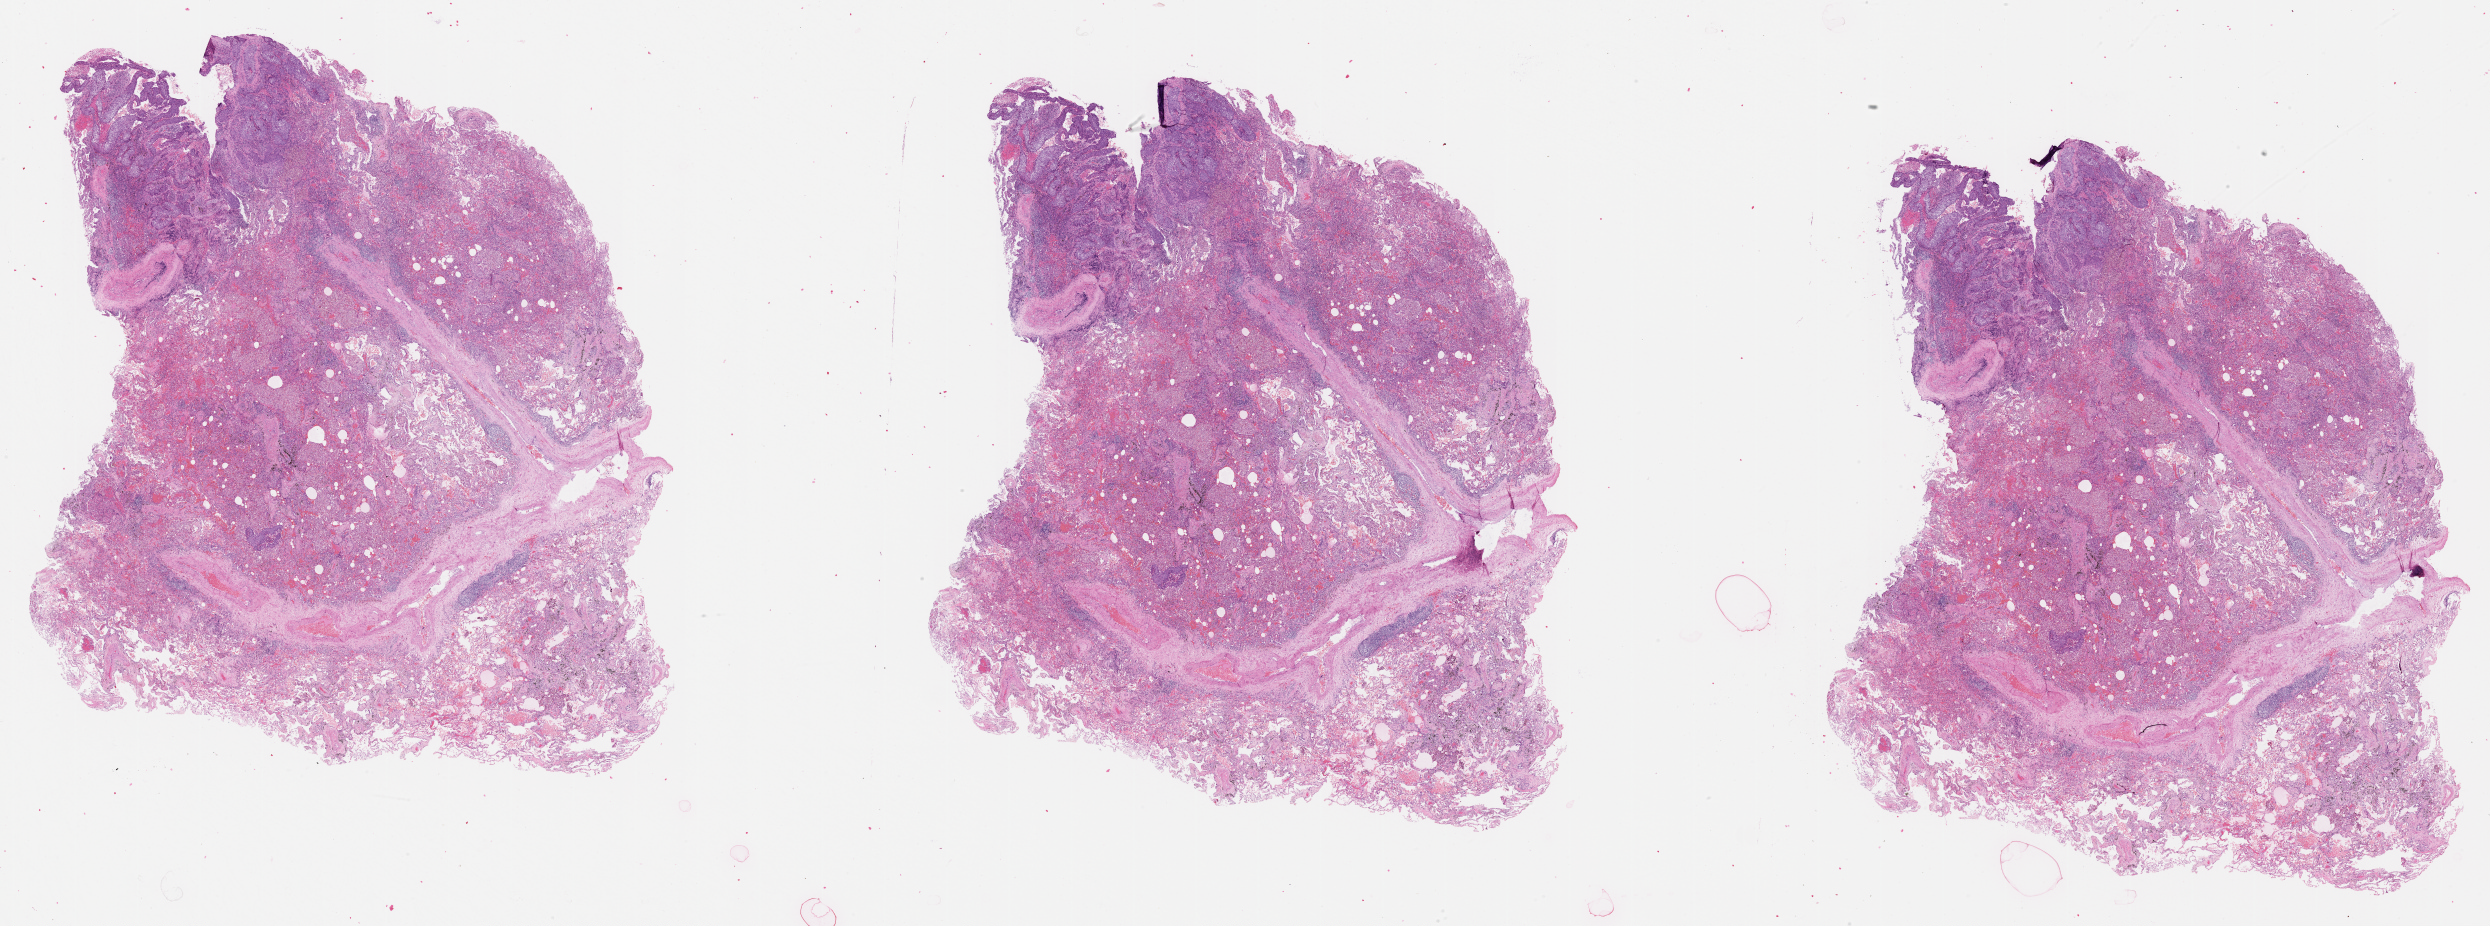
Digitized H&E tissue section (whole slide), a low-resolution overview of the entire scanned area, about 40.1 x 14.9 mm. Lung, tumour tissue. 57-year-old male patient.
• patient diagnosis (cohort enrolment): squamous cell carcinoma (lung)